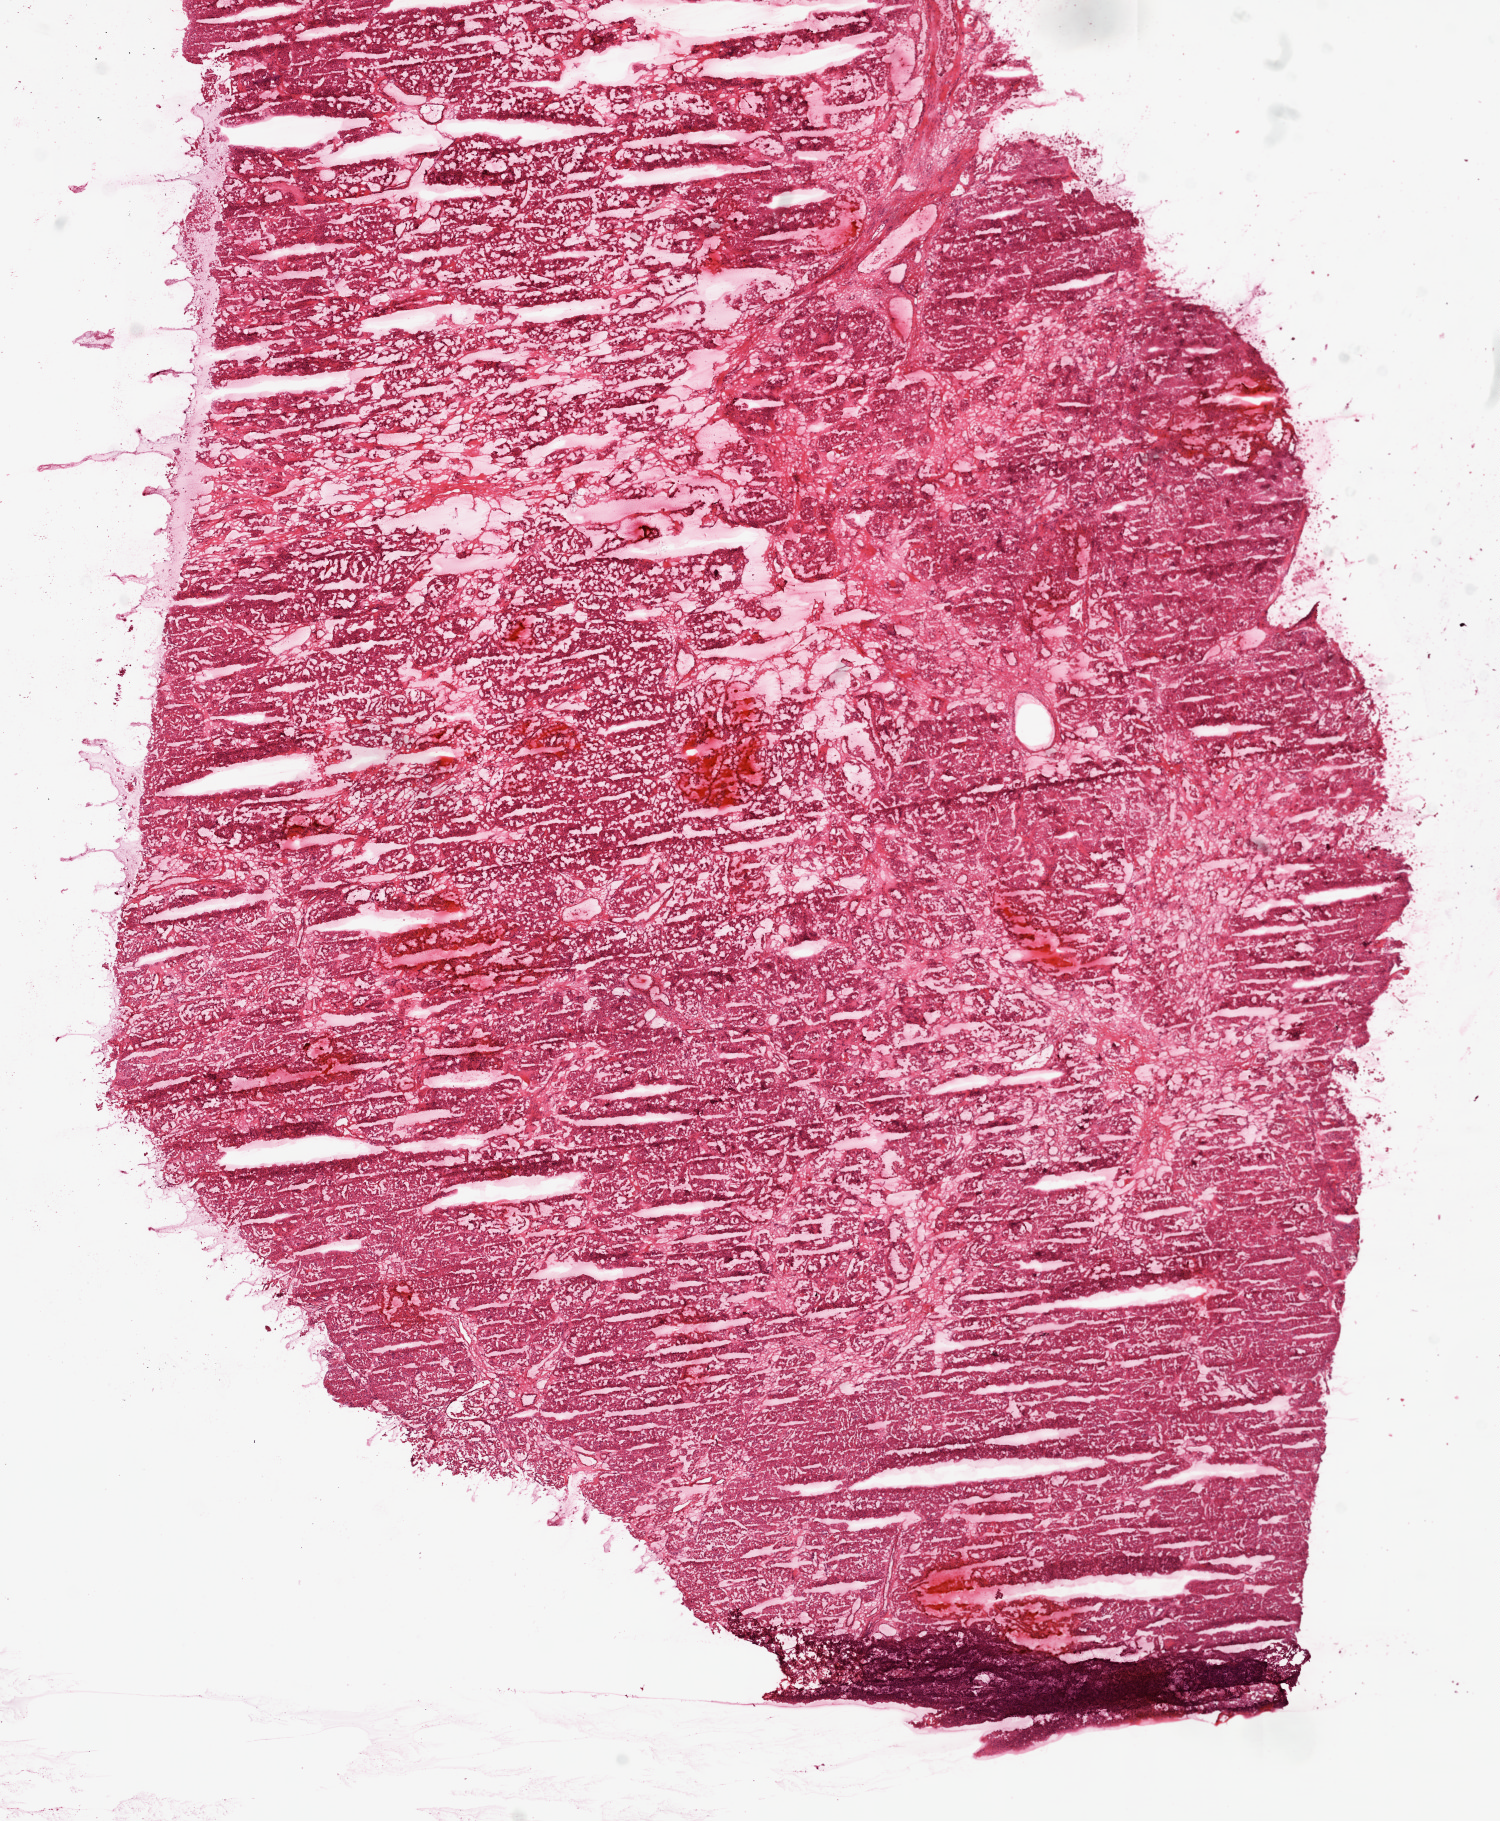
Digitized H&E tissue section (whole slide) — low-resolution overview of the scanned area, about 12.0 x 14.6 mm (acquisition: 20x scan). Frozen section from the top of the tissue portion. Sample: primary tumour, kidney. Male, age 49 years at initial diagnosis. Histologic grade: G3 (poorly differentiated). Pathologist review of this section (percent, as recorded): tumour cells 90%, tumour nuclei 90%, normal cells 0%, stromal cells 10%, necrosis 0%.
Diagnosis: Clear cell adenocarcinoma, NOS. Laterality: right. AJCC pathologic stage: I.